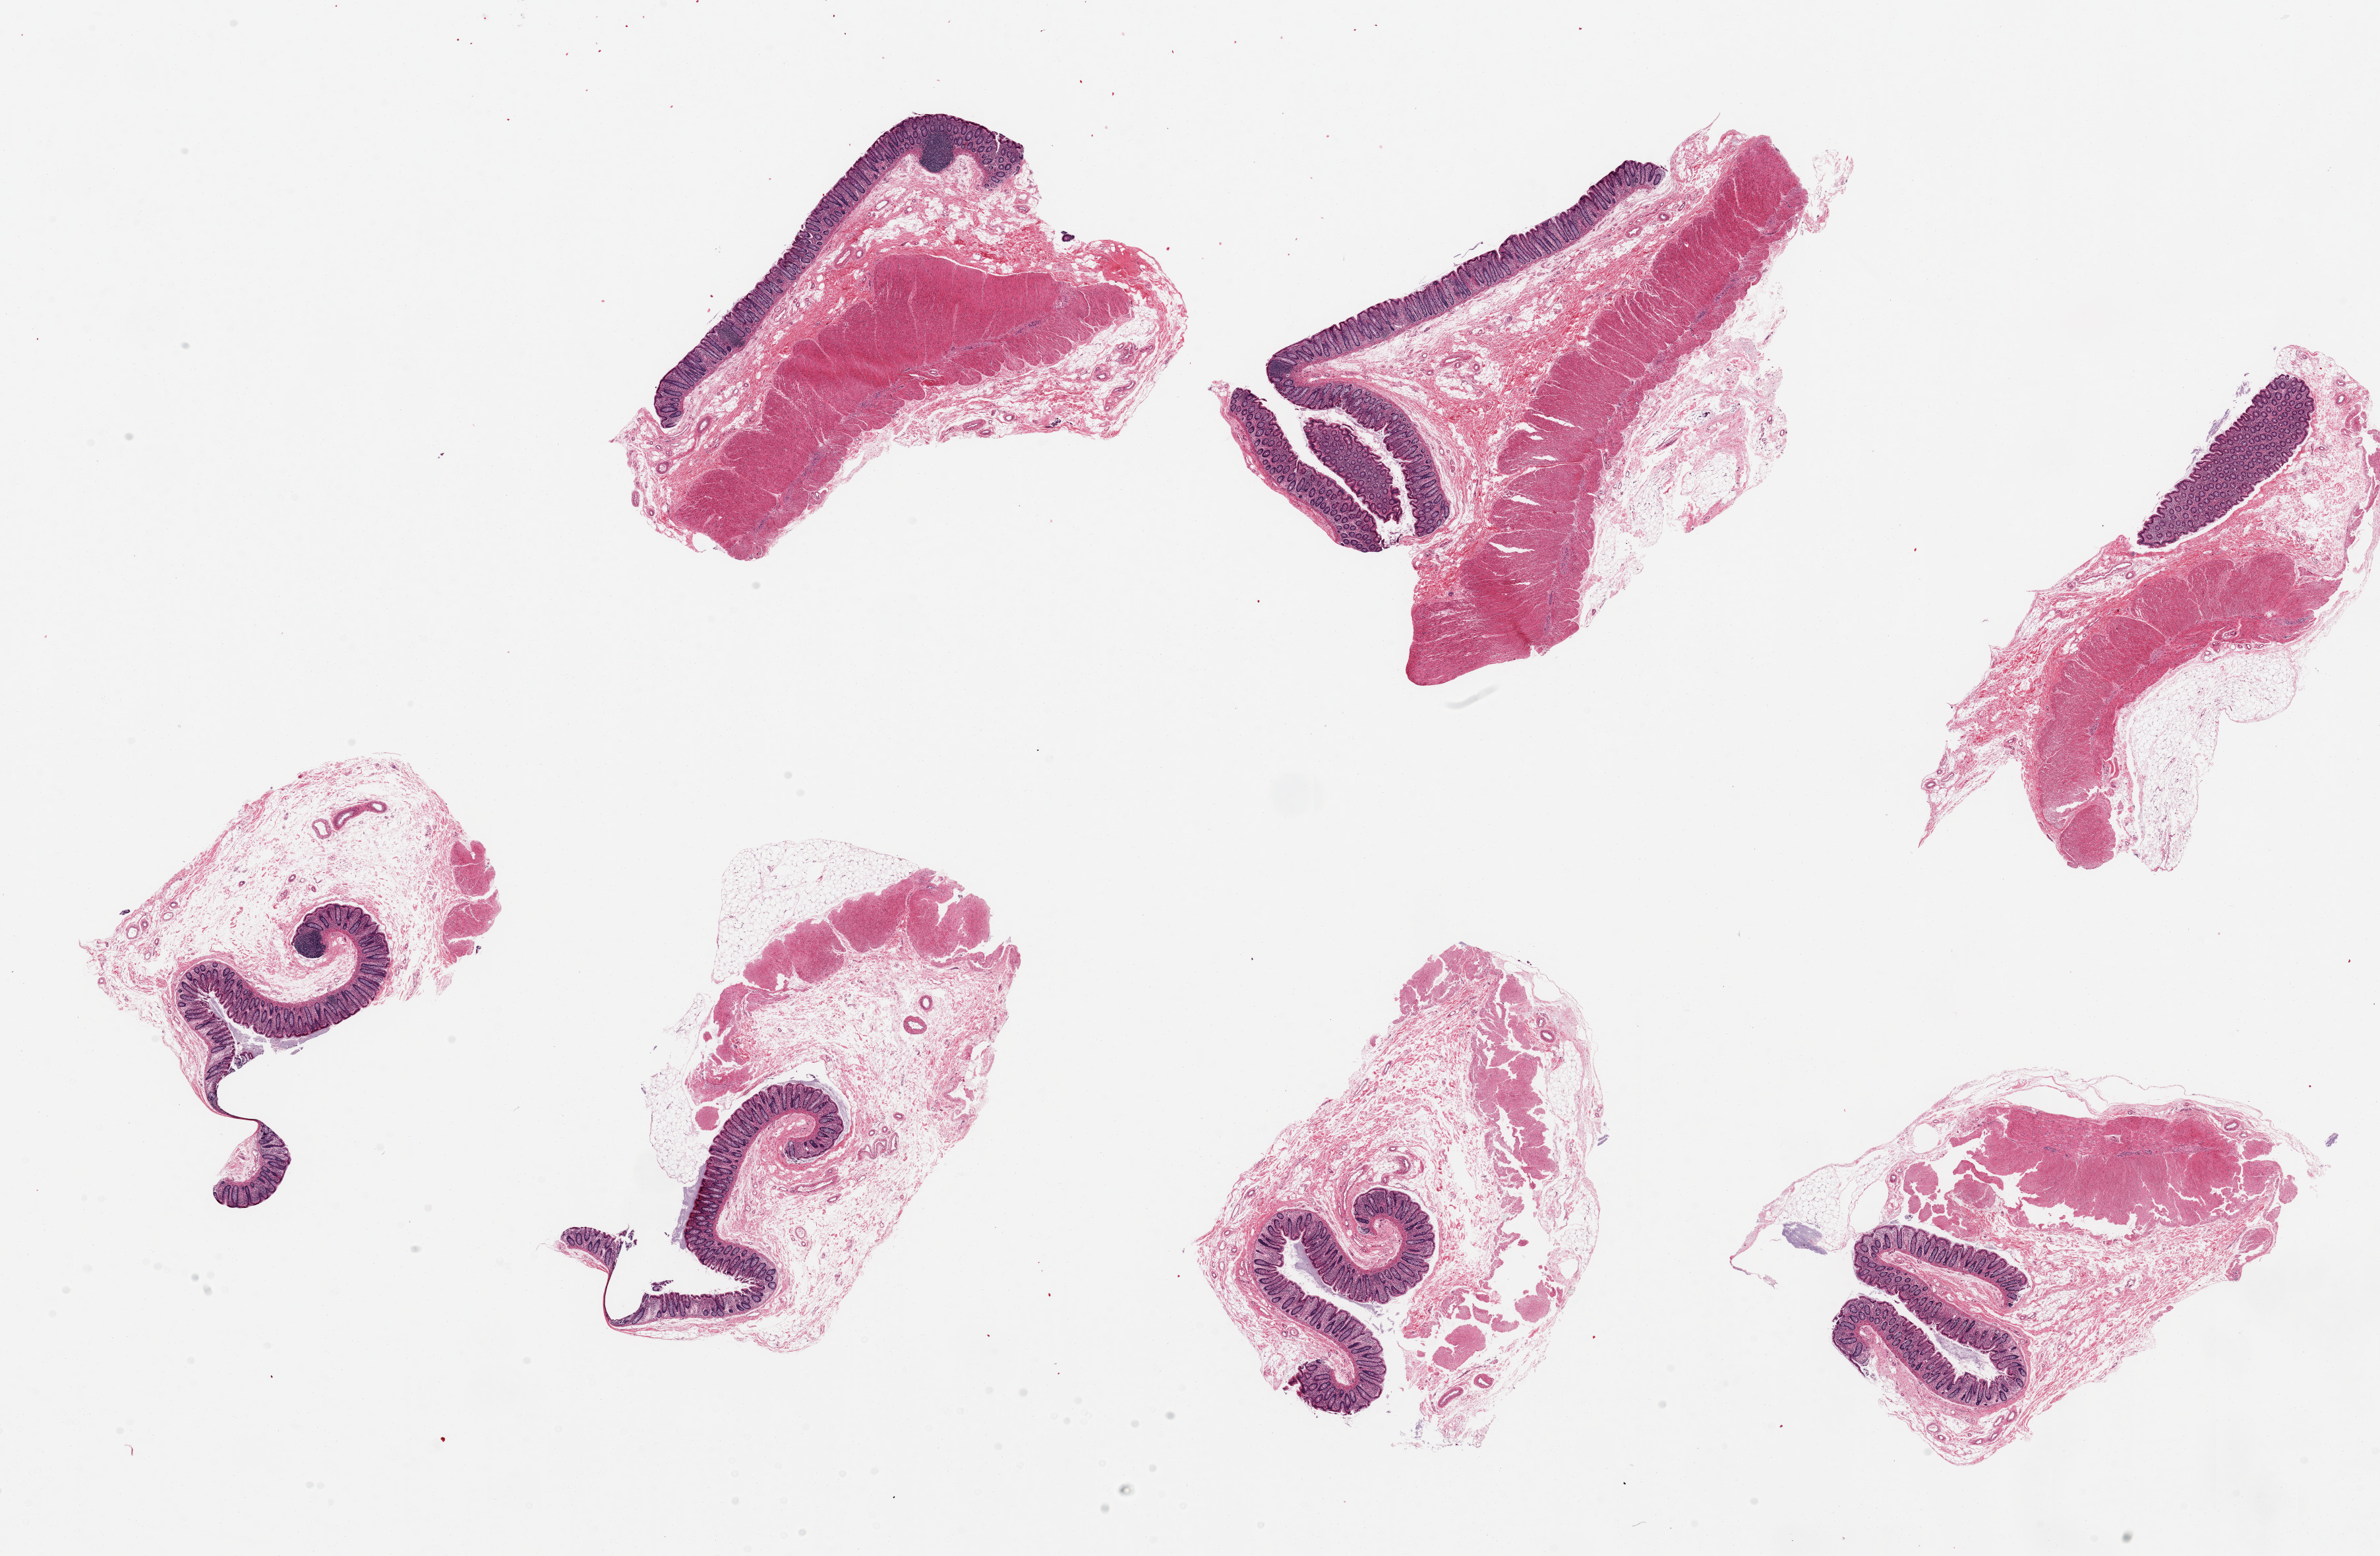
Whole-slide image, hematoxylin and eosin (H&E) stain — whole scanned area (about 28.5 x 18.7 mm) shown as a low-resolution overview, PAXgene-fixed paraffin-embedded (PFPE) section, target tissue: transverse colon, donor tissue sample.
* pathologist's review note for this sample: 6 pieces, ~7x3.5mm. Mucosa reasonably well preserved, ~8-10% of thickness